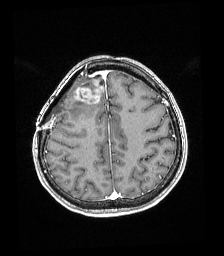
Brain MRI from a brain-tumour surgery series, one axial slice. Position 60 of 192 along the scan axis. T1-weighted post-contrast. 1 mm slice thickness. 224 × 256 image matrix. Case-level facts recorded for this patient, not image findings: histopathology: Astrocytoma; WHO grade: 4; IDH mutation: yes; tumour location: Right superficial frontal.
Outlined on this slice (manually delineated by an expert):
- tumour: box from (x=72, y=80) to (x=105, y=104) px